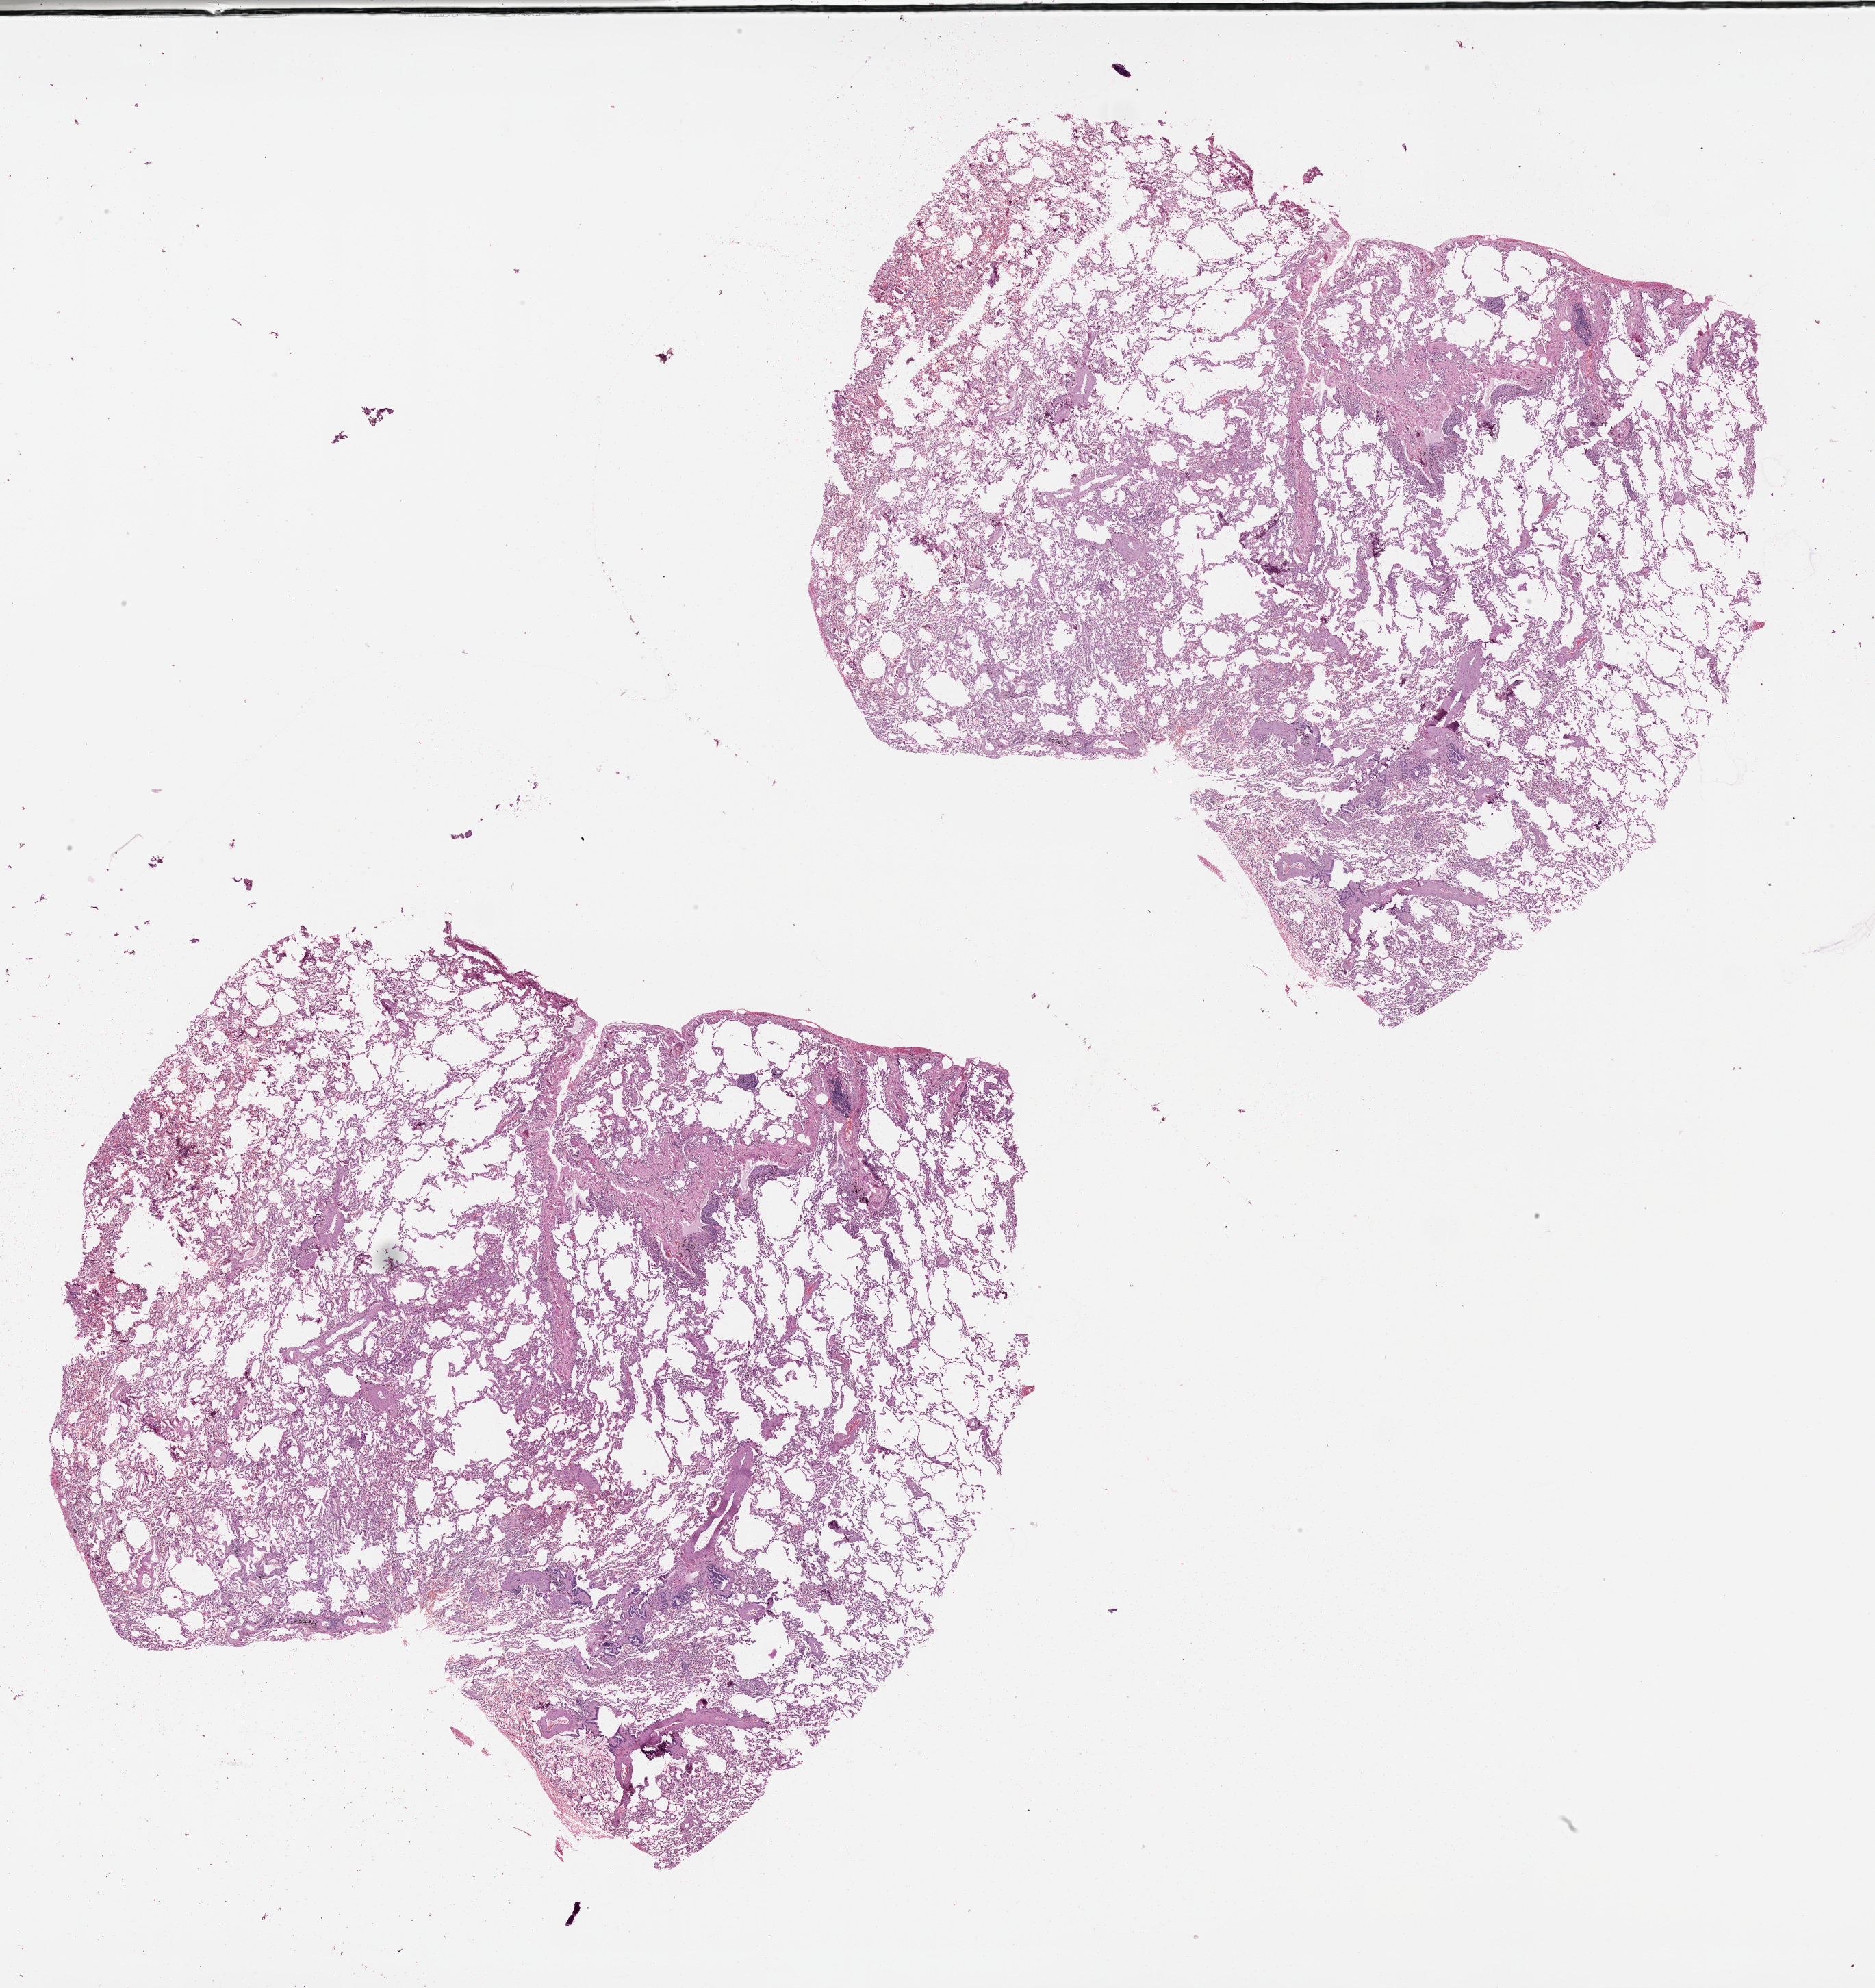
Hematoxylin and eosin (H&E) stained whole-slide image, whole scanned area (about 22.0 x 23.4 mm, from a 20x scan) shown as a low-resolution overview; lung, normal (non-tumour) tissue. 63-year-old male patient.
This section: normal (non-tumour) tissue from the same patient. Patient diagnosis (cohort enrolment): squamous cell carcinoma (lung).